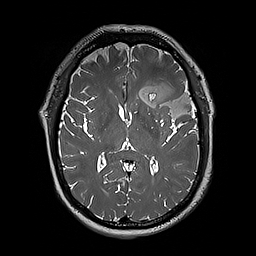
Brain MRI from a brain-tumour surgery series, one axial slice; slice 108 of 192 in the series (ordered by position); 1 mm slice thickness; 256 × 256 image matrix. From the clinical record (not read from this slice): histopathology: Oligodendroglioma; WHO grade: 3; IDH mutation: yes; tumour location: Left Sylvian Fissure (Temporal).
Annotated regions visible in this slice (expert manual segmentation):
- tumour: bounding box <124,80,197,119> (left, top, right, bottom; pixels)